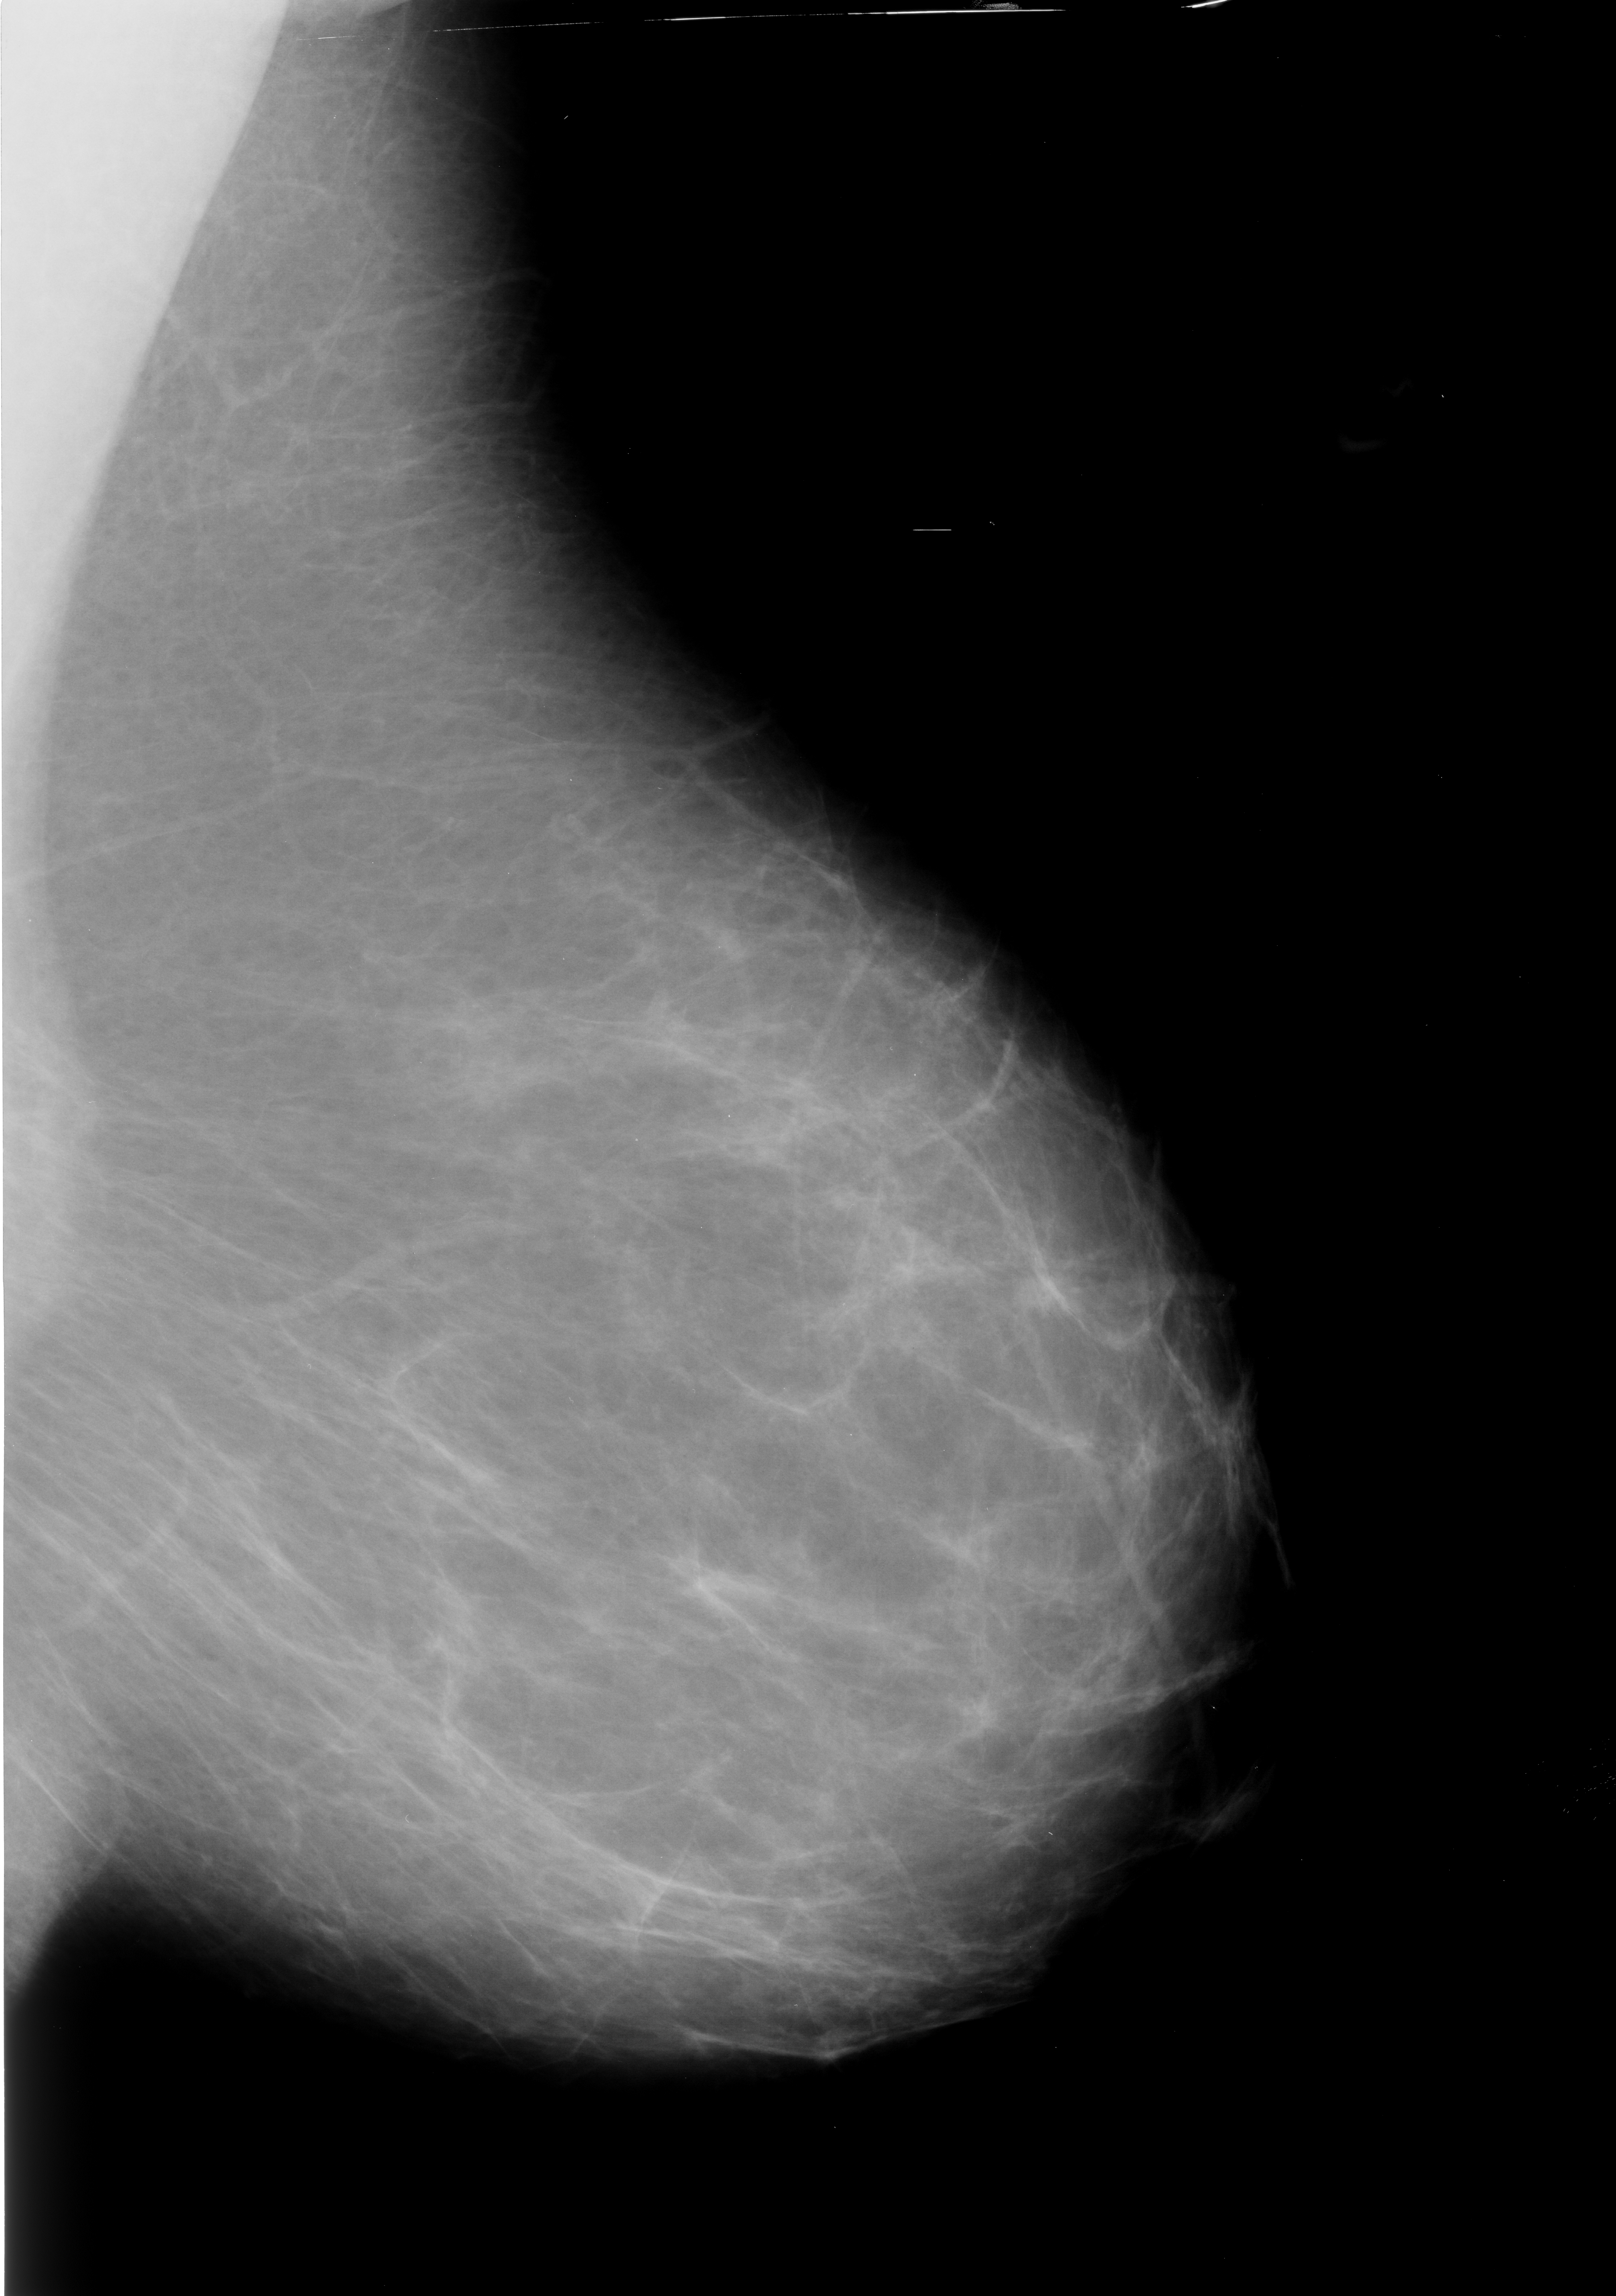
Digitized screen-film mammogram; left breast; MLO view; breast composition: almost entirely fatty (BI-RADS density category 1 of 4); 1616 × 2296 image matrix.
Marked abnormalities (boxes around the expert regions of interest):
- mass, shape irregular, margins spiculated; BI-RADS assessment category 4; pathology (as recorded): malignant: bounding box <1011,1243,1090,1329> (left, top, right, bottom; pixels)